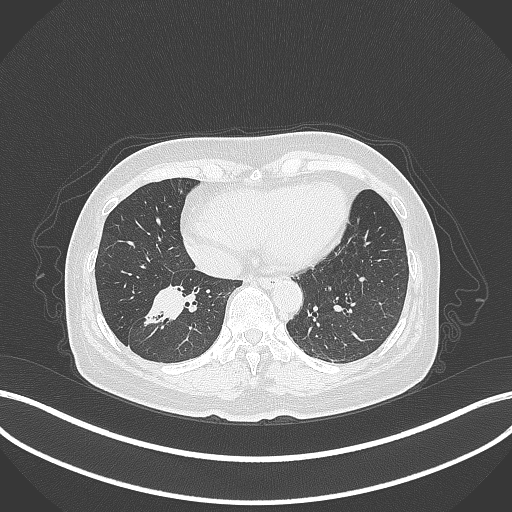
Chest CT, one axial slice. Position 128 of 429 along the scan axis. Reconstruction kernel B70f. Lung window (W 1500 / L -600 HU). 512 × 512 image matrix, field of view 400 × 400 mm. Patient: female, 67 years. From the clinical record (not read from this slice): clinical TNM (as recorded): T1c N1 M0.
Outlined on this slice (rectangle marked by the reading radiologist):
- lung tumour (recorded histology: adenocarcinoma): box from (x=143, y=281) to (x=195, y=328) px